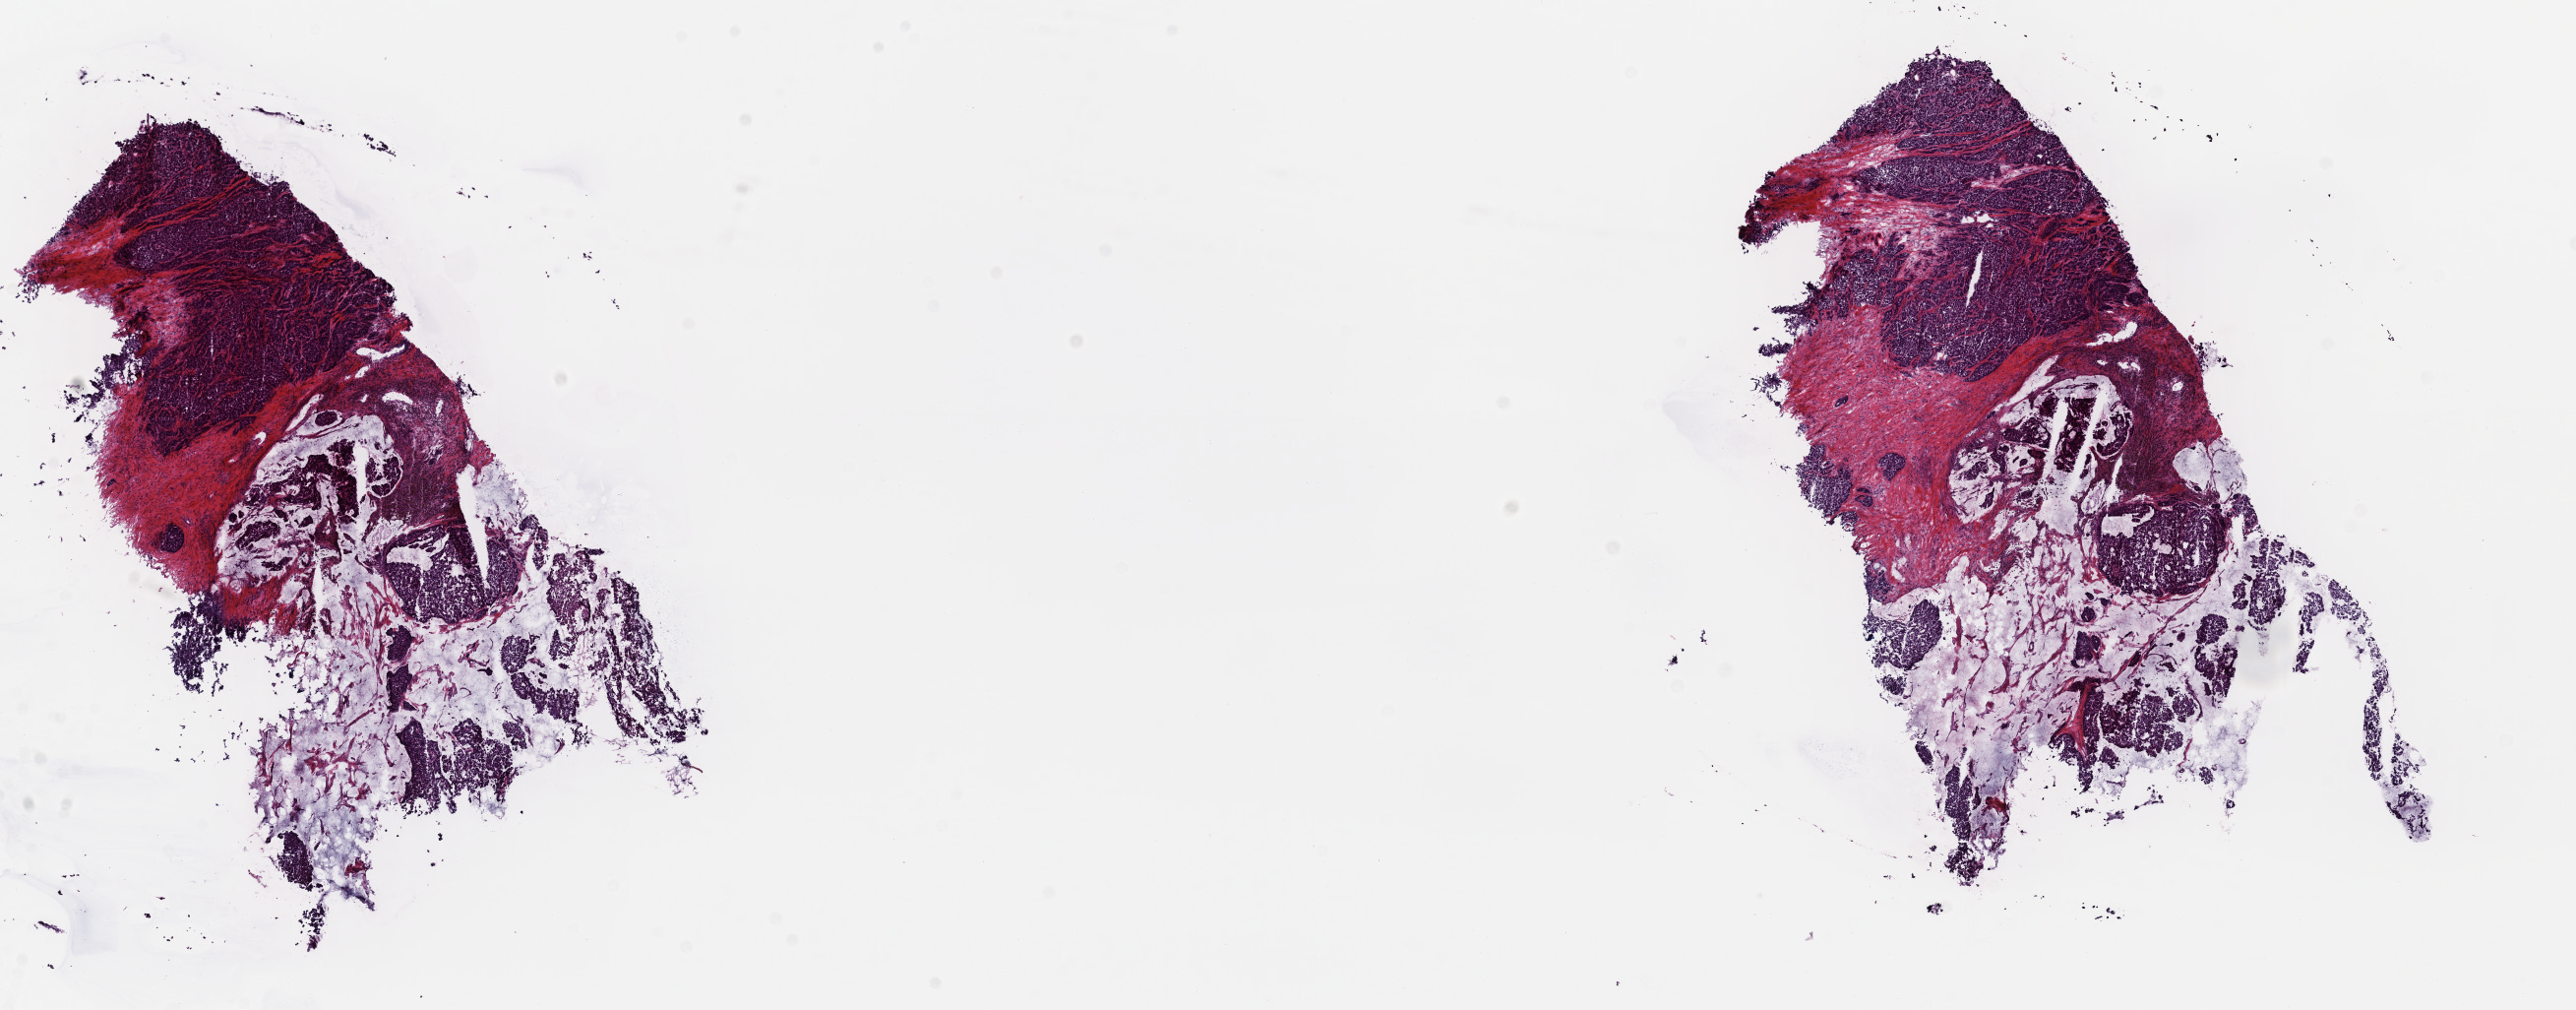
Whole-slide histology image, H&E, whole scanned area (about 20.7 x 8.1 mm, acquisition: 40x scan) shown as a low-resolution overview; frozen section from the top of the tissue portion; sample: primary tumour, breast. Female patient; age at initial diagnosis 84 years.
Histologic diagnosis: Mucinous adenocarcinoma.